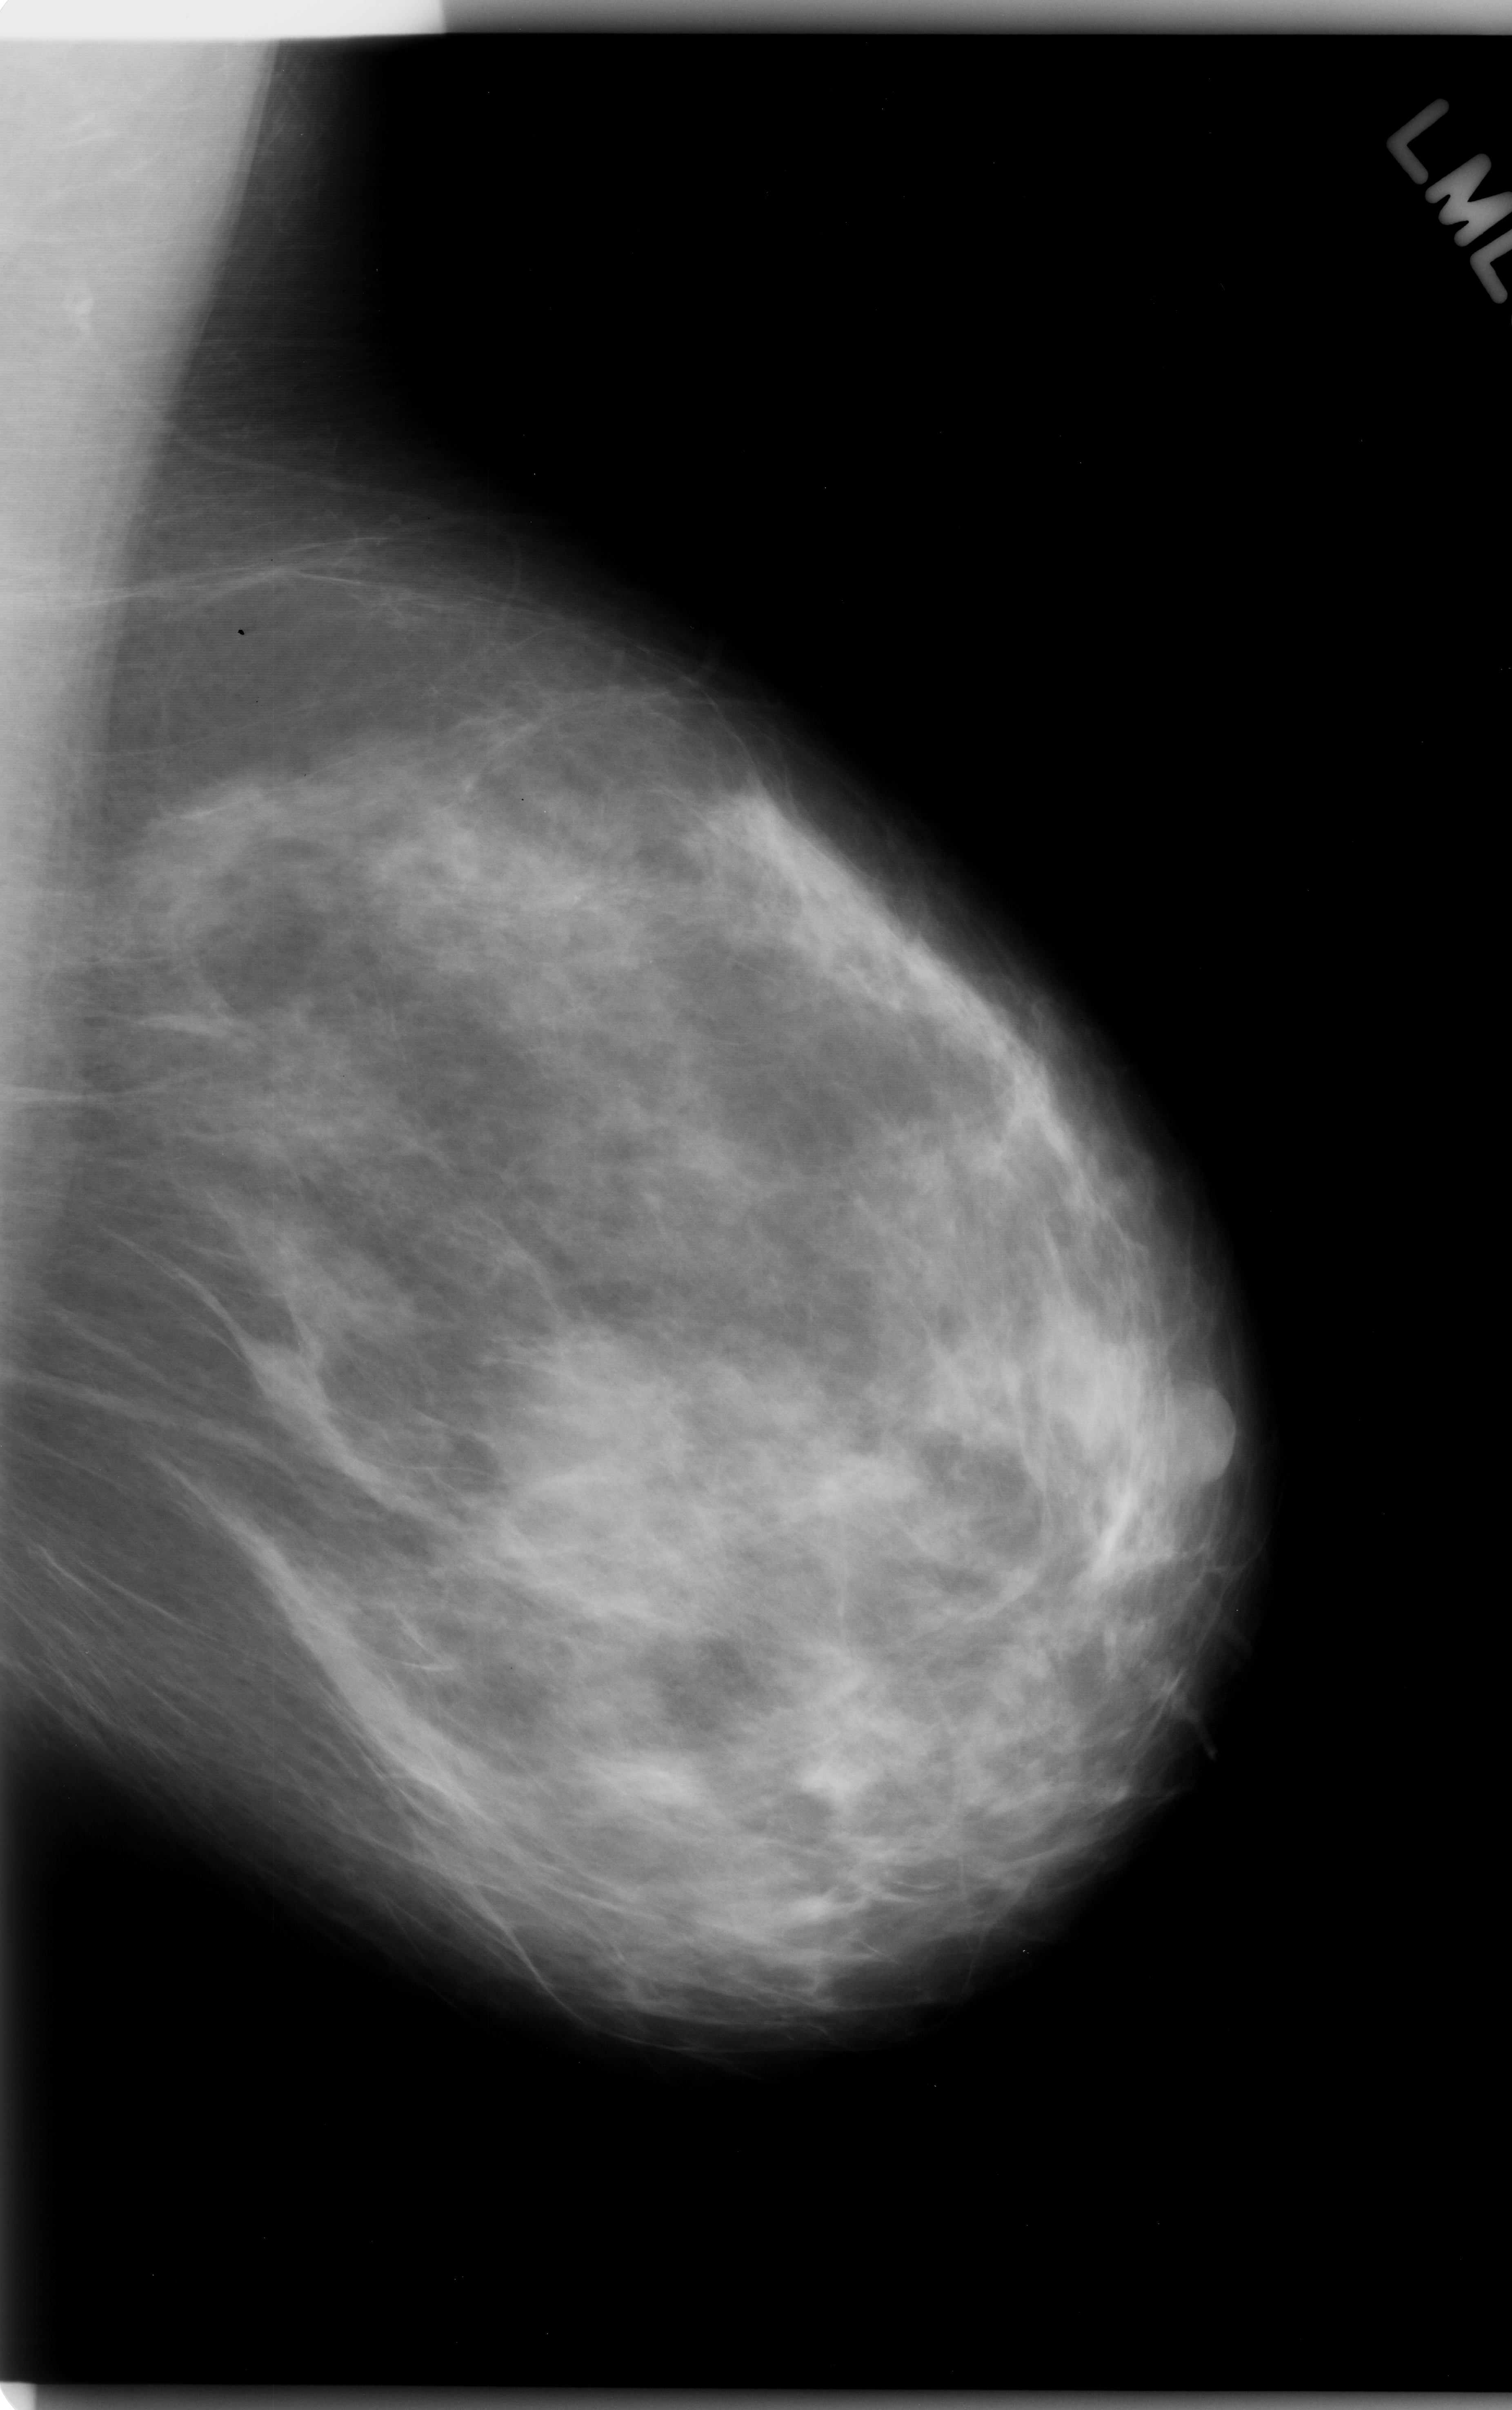
Digitized screen-film mammogram; left breast; MLO view; BI-RADS breast density category 2 (scale 1–4); 1512 × 2410 image matrix.
Marked abnormalities (boxes around the expert regions of interest):
- calcifications, morphology pleomorphic, distribution clustered; BI-RADS assessment category 4; pathology (as recorded): malignant: box from (x=372, y=757) to (x=781, y=1059) px